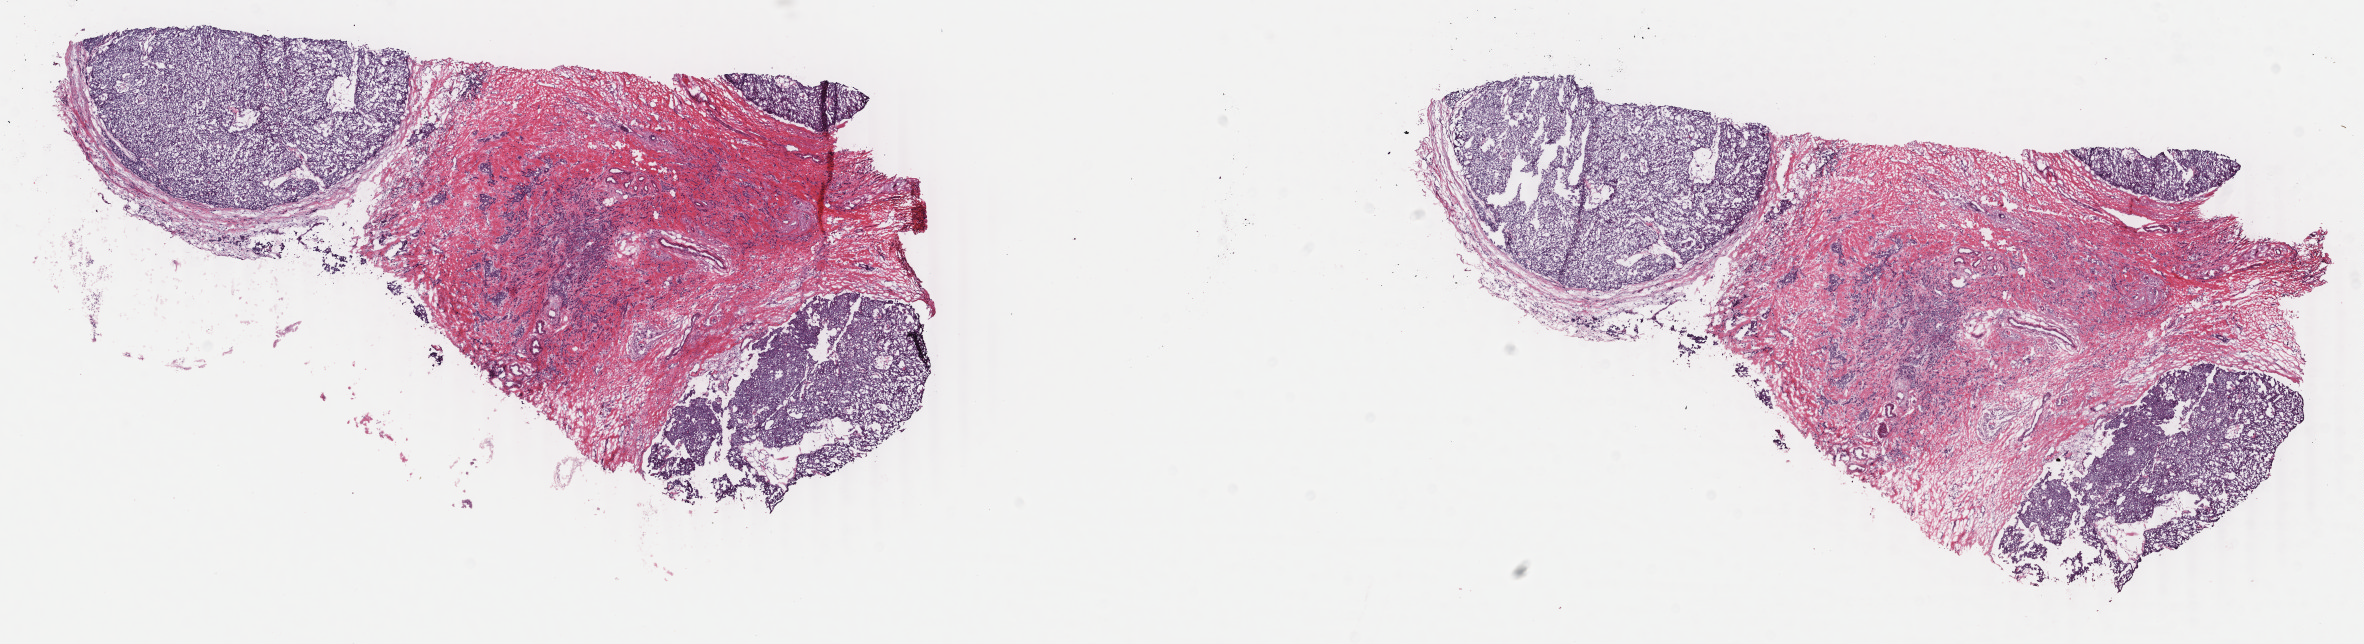
Whole-slide histology image, Hematoxylin and eosin (H&E) stained — low-resolution overview of the scanned area, about 18.8 x 5.1 mm (acquisition: 40x scan). Frozen section from the top of the tissue portion. Primary tumour sample from the breast. Patient: female, age at initial diagnosis 54 years. Slide review estimates, as recorded: tumour cells 85%, tumour nuclei 85%, normal cells 0%, stromal cells 14%, necrosis 1%. Infiltration values recorded for this section: lymphocyte infiltration 2%, monocyte infiltration 0%, neutrophil infiltration 0%.
Lymph nodes positive (case pathology): 1 of 17 examined. Laterality: left. Pathologic diagnosis: Infiltrating duct carcinoma, NOS. AJCC pathologic stage: IIIA. TNM: T2 N2 M0.